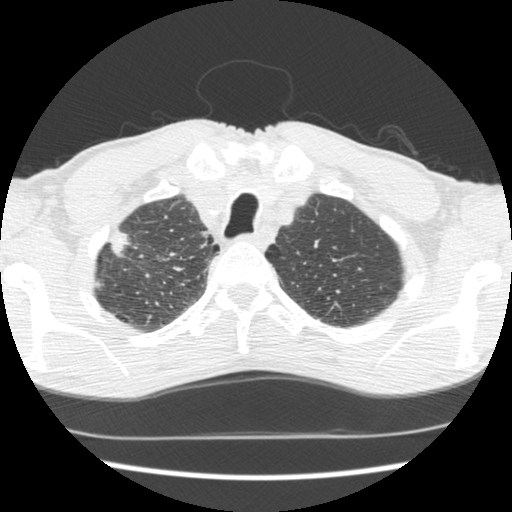
Axial slice from a low-dose chest CT screening exam, first (baseline) screen, lung window (W 1500 / L -600 HU), standard (soft-tissue) reconstruction kernel (STANDARD), slice 33 of 197 in the series, 512 × 512 image matrix, field of view 318 × 318 mm. Male participant, aged 62 years at enrolment. Current smoker at enrolment.
Expert-annotated lung lesion, box from (x=92, y=223) to (x=143, y=273) px. Screening reader's record for this exam: no non-calcified nodule ≥4 mm recorded. Participant outcome: lung cancer diagnosed 640 days after this screen — adenocarcinoma, NOS, right upper lobe, poorly differentiated (G3), stage IIA (AJCC 6th edition), 22 mm at pathology.